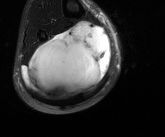
MRI of an extremity soft-tissue mass, one axial slice; position 64 of 81 along the scan axis; T2-weighted fat-saturated; MR volume resampled by the dataset authors to the PET/CT grid (not the native acquisition matrix); 3.27 mm slice thickness; 165 × 137 image matrix. Male patient. Case-level facts recorded for this patient, not image findings: histological type: liposarcoma - round cell; grade: high; site of the primary tumour: right calf.
Structures marked on this image (expert contour drawn on MRI and transferred to this co-registered scan by the dataset authors):
- gross tumour volume (mass): bounding box <21,21,111,101> (left, top, right, bottom; pixels)